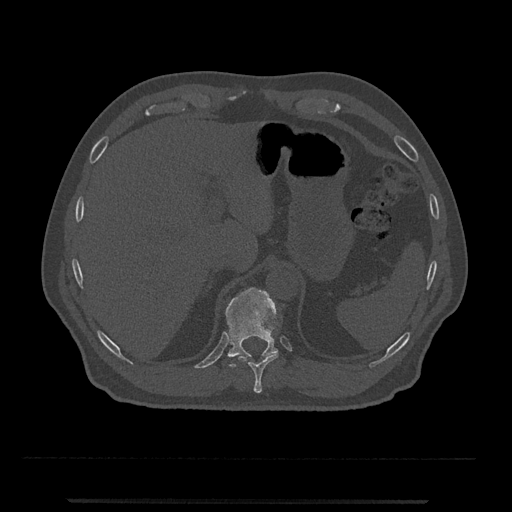
CT including the spine, one axial slice; slice 489 of 797 in the series (ordered by position); reconstruction kernel Br40s/3; 120 kVp; bone window (W 1800 / L 400 HU); 0.5 mm slice thickness; 512 × 512 image matrix, field of view 419 × 419 mm. Patient: male, 63 years. From the clinical record (not read from this slice): primary cancer: prostate.
Annotated regions visible in this slice (semi-automatically segmented with operator editing):
- T10 vertebra: bounding box [x1, y1, x2, y2] px = [239, 353, 278, 393]
- T11 vertebra: [225, 287, 278, 367]